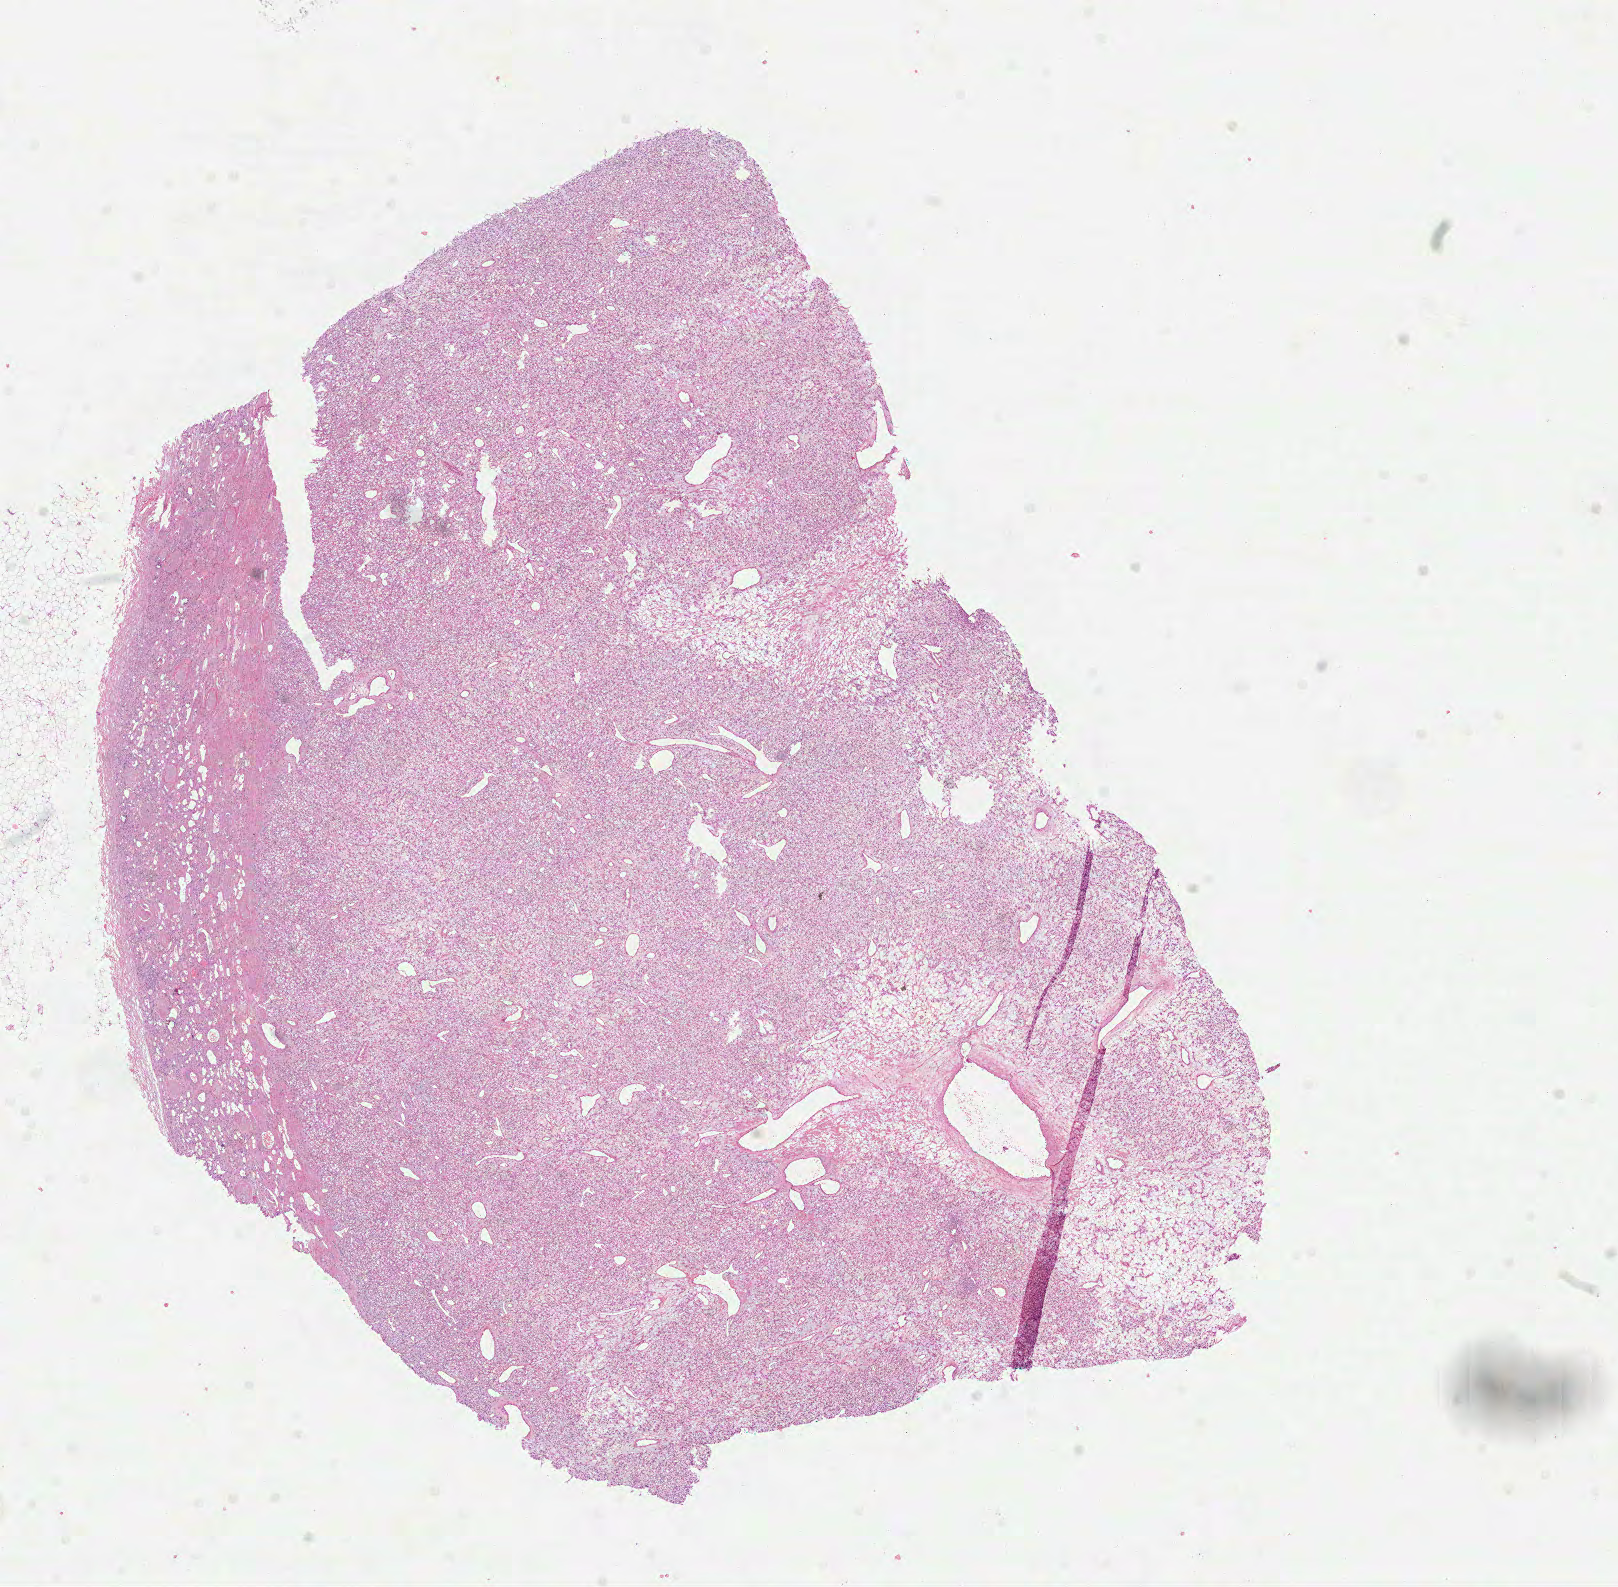
Hematoxylin and eosin (H&E) stained whole-slide image, shown as a low-resolution overview of the whole scanned area (about 13.1 x 12.8 mm, from a 40x scan). Formalin-fixed paraffin-embedded (FFPE) diagnostic section. Sample: primary tumour, kidney. Male patient; age at initial diagnosis 51 years. Histologic grade: G2 (moderately differentiated).
Histologic diagnosis: Clear cell adenocarcinoma, NOS. AJCC pathologic stage: I.